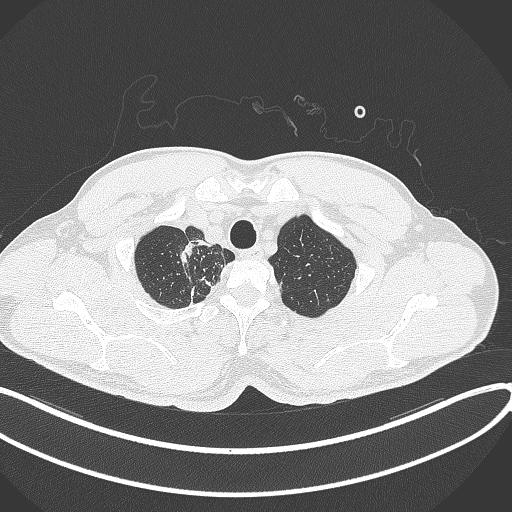
Chest CT, one axial slice. Slice 337 of 391 in the series (ordered by position). Reconstruction kernel B70f. 120 kVp. Lung window (W 1500 / L -600 HU). 1 mm slice thickness. 512 × 512 image matrix. Male patient, age 48 years. From the clinical record (not read from this slice): clinical TNM (as recorded): T1c N1 M1.
Outlined on this slice (bounding box drawn by a radiologist):
- lung tumour (recorded histology: adenocarcinoma): bounding box [x1, y1, x2, y2] px = [175, 238, 198, 264]